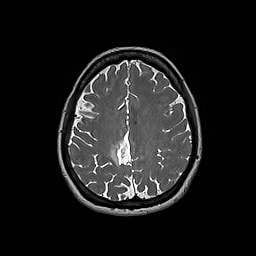
Brain MRI from a brain-tumour surgery series, one axial slice. Position 66 of 192 along the scan axis. 256 × 256 image matrix, field of view 250 × 250 mm. Case-level facts recorded for this patient, not image findings: histopathology: Oligodendroglioma; WHO grade: 2.
Outlined on this slice (expert manual segmentation):
- tumour: box from (x=110, y=143) to (x=120, y=165) px